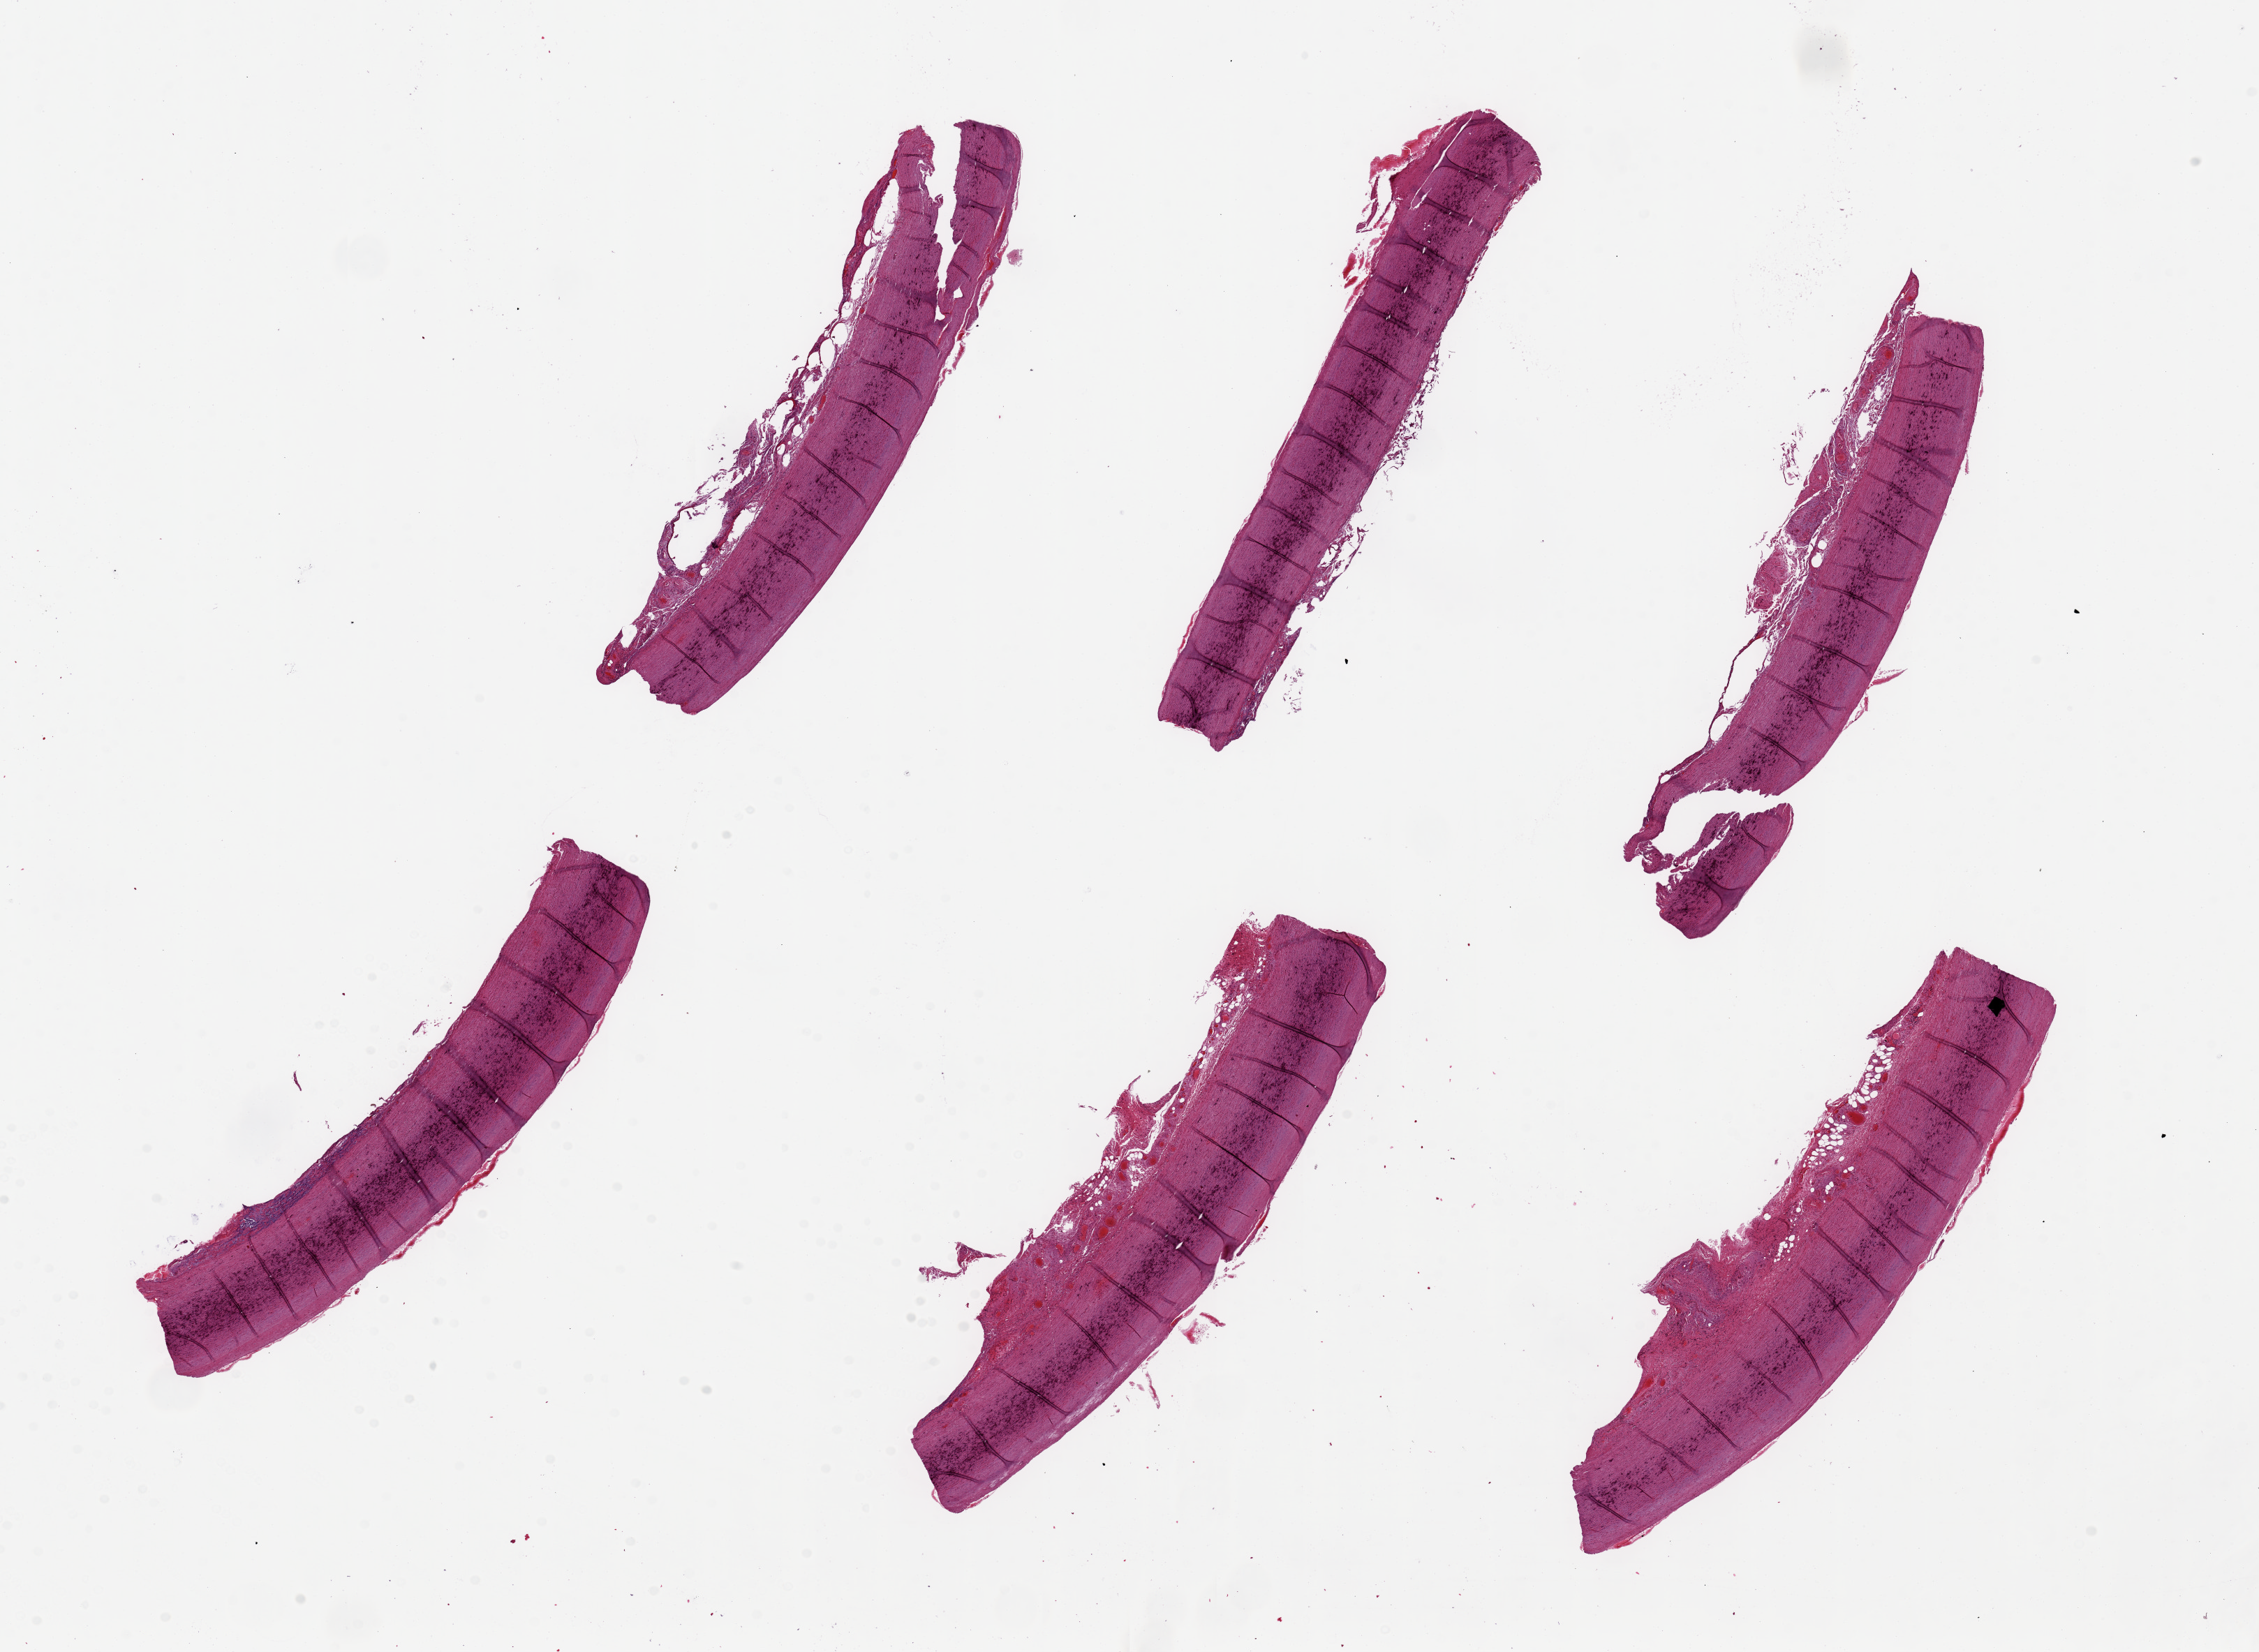
Whole-slide image, H&E stain, brightfield — a low-resolution overview of the entire scanned area, about 25.6 x 18.7 mm; PAXgene-fixed paraffin-embedded (PFPE) section; sampled site (target tissue): aorta; donor tissue sample. Donor: male.
Pathologist's review note for this sample: 6 pieces, up to 8x2mm; fine medial calcification, no plaques.